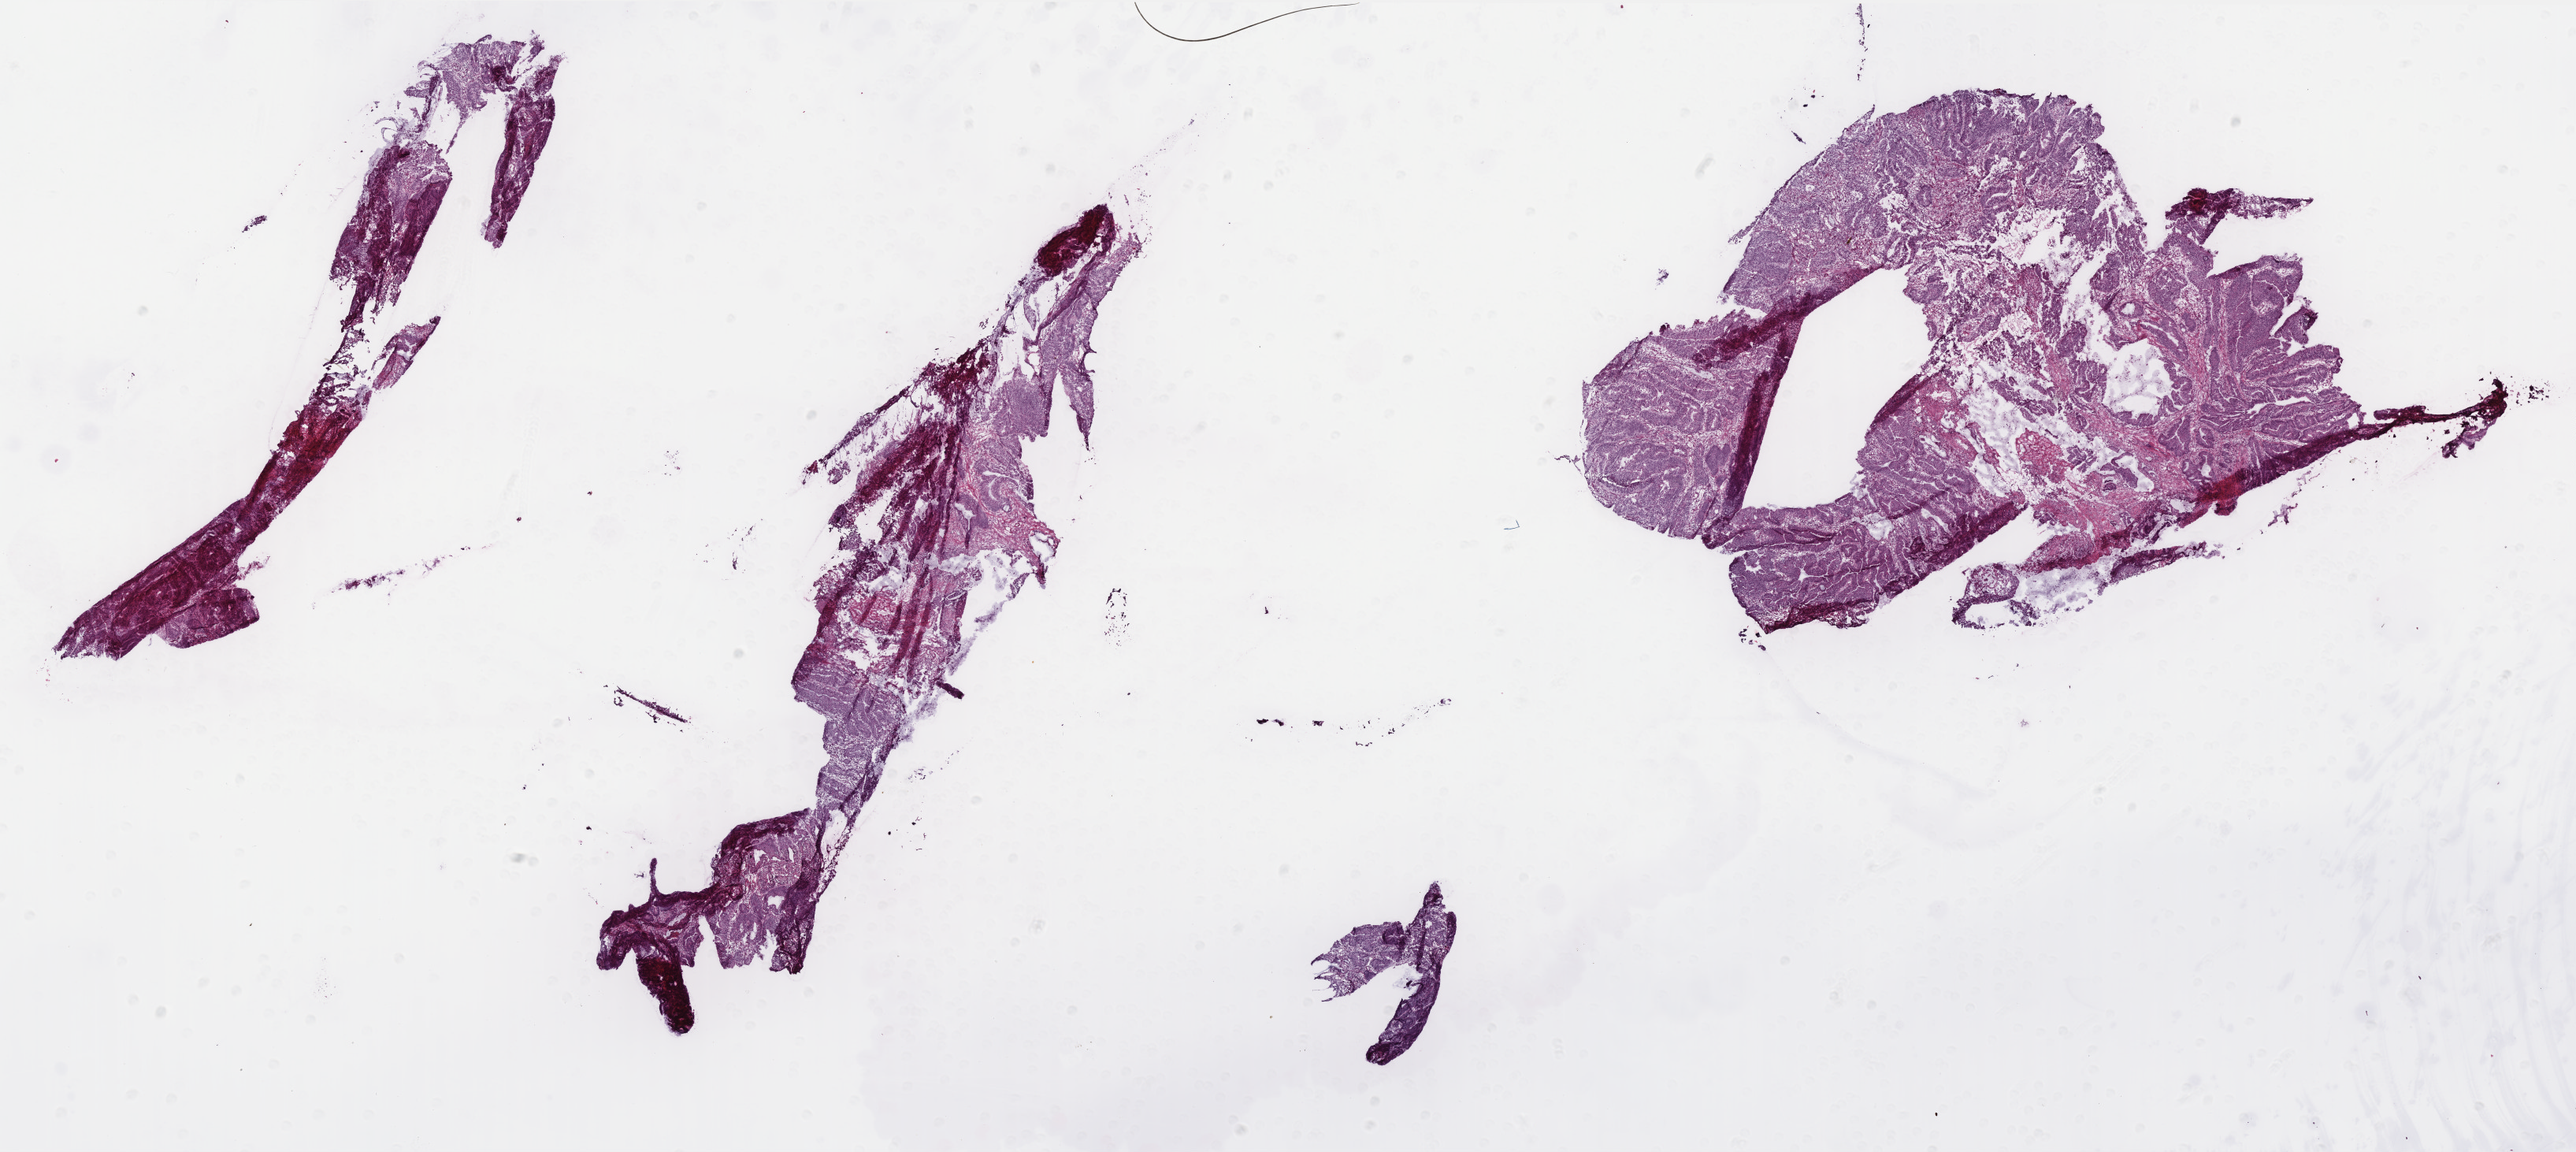
Hematoxylin and eosin (H&E) stained whole-slide image, shown as a low-resolution overview of the whole scanned area (about 26.2 x 11.7 mm, from a 40x scan), frozen section, rectum, primary tumour sample. Female, age 57 years at initial diagnosis. Pathologist review of this section (percent, as recorded): tumour cells 93%, tumour nuclei 85%, normal cells 0%, stromal cells 6%, necrosis 1%. Infiltration values recorded for this section: lymphocyte infiltration 7%, monocyte infiltration 1%, neutrophil infiltration 3%.
AJCC pathologic stage: III. Lymph nodes positive (case pathology): 1 of 12 examined. Pathologic diagnosis: Mucinous adenocarcinoma.